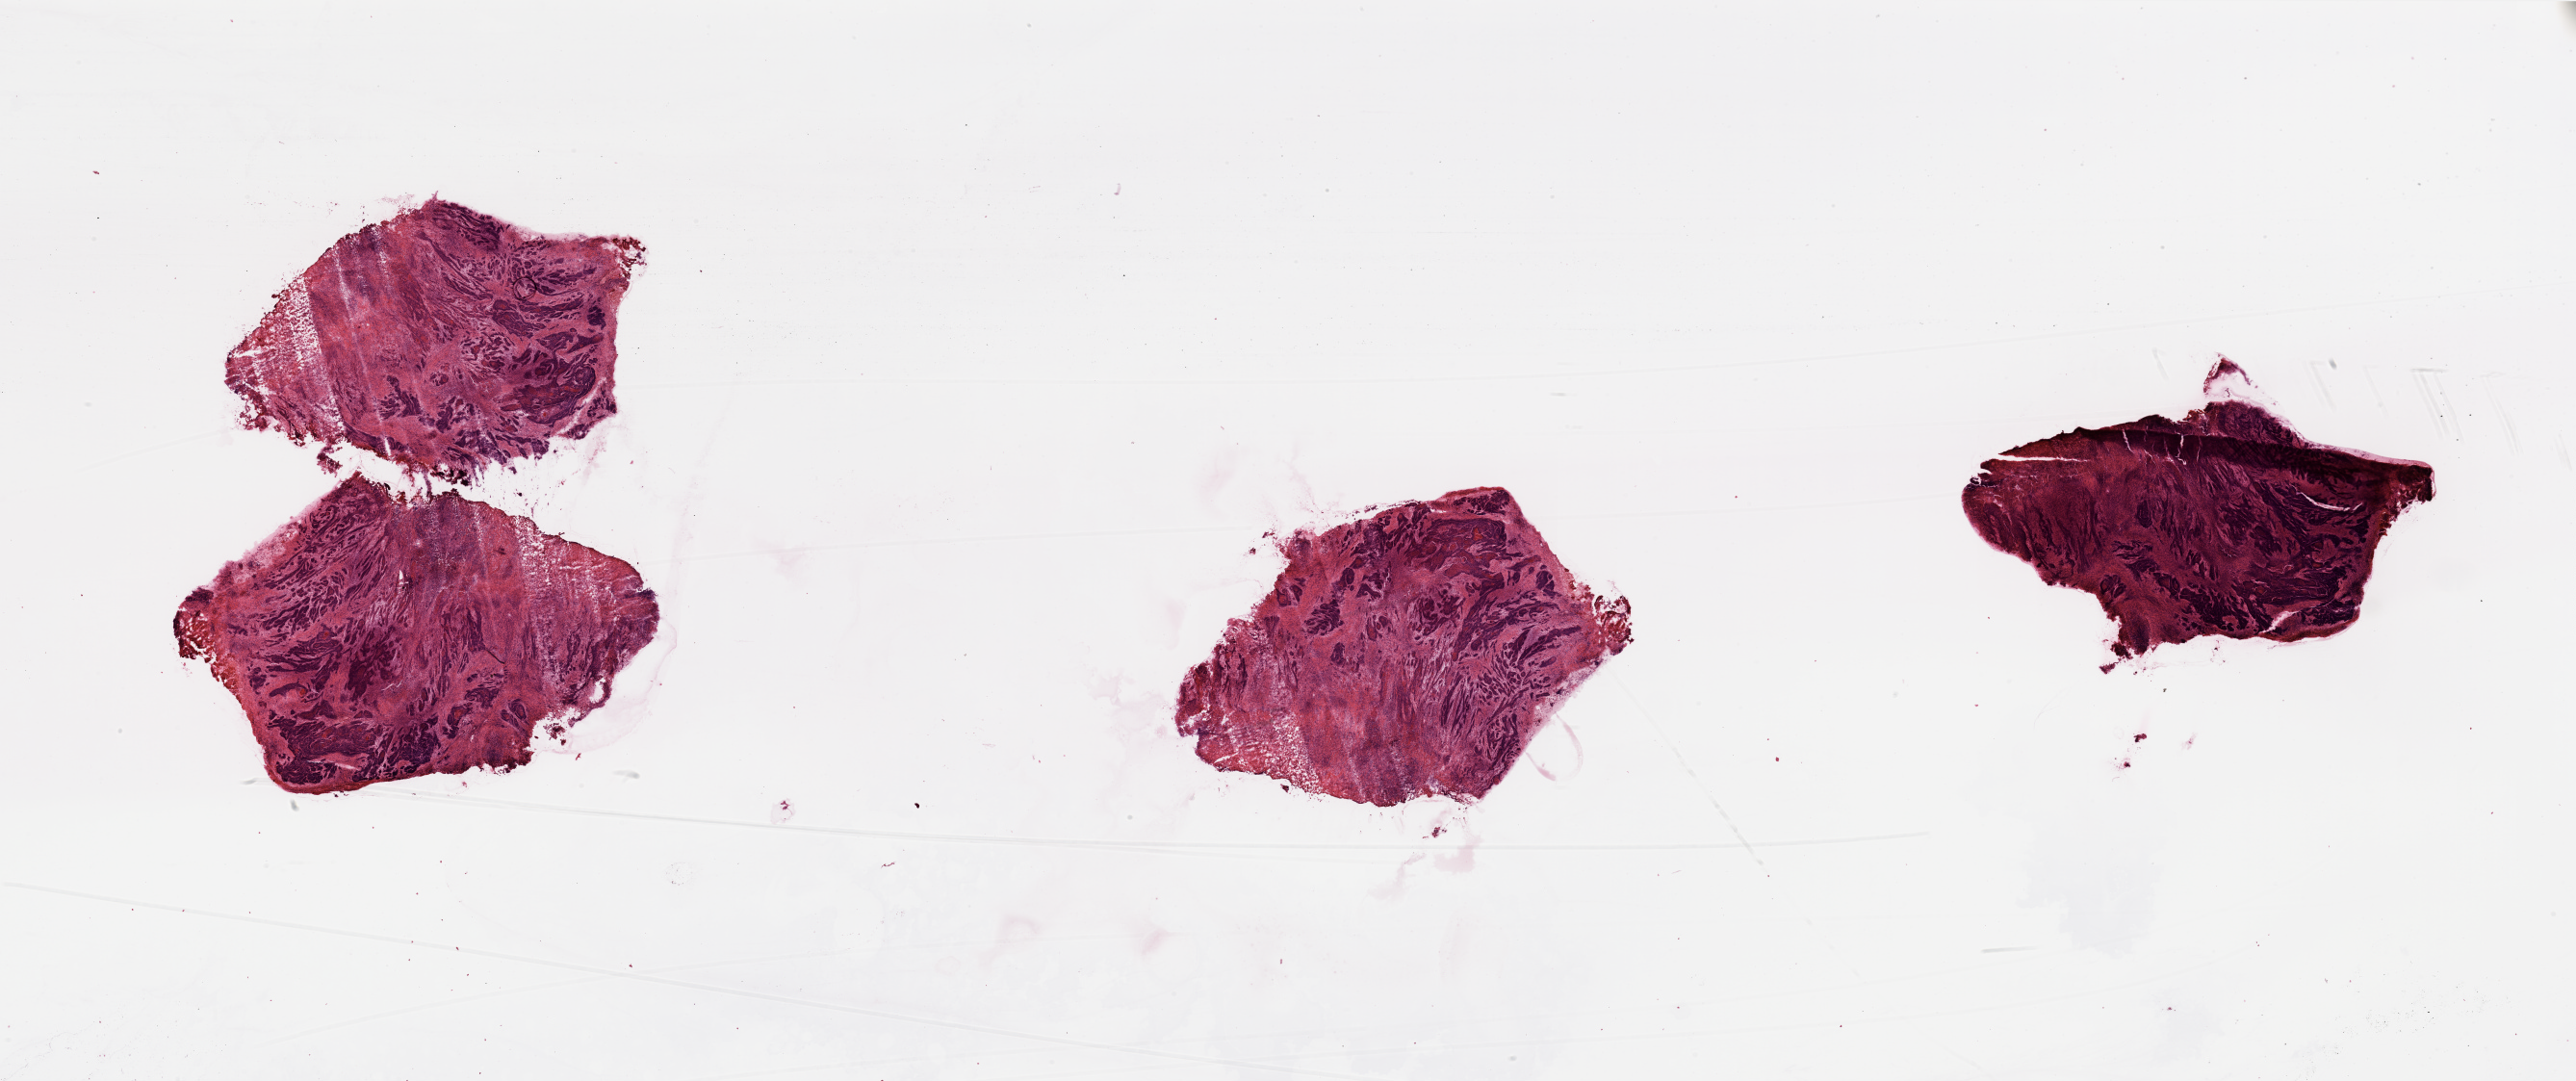
Hematoxylin and eosin (H&E) stained whole-slide image, whole scanned area (about 42.3 x 17.8 mm, acquisition: 20x scan) shown as a low-resolution overview, tumour tissue sample, sampled site: tongue. Patient: male, age 53 years. Histologic grade: G2 (moderately differentiated). Pathologist review of this section (percent, as recorded): tumour nuclei 85%, necrosis 20%.
AJCC pathologic stage: IVA. Histologic diagnosis: Squamous cell carcinoma, NOS.